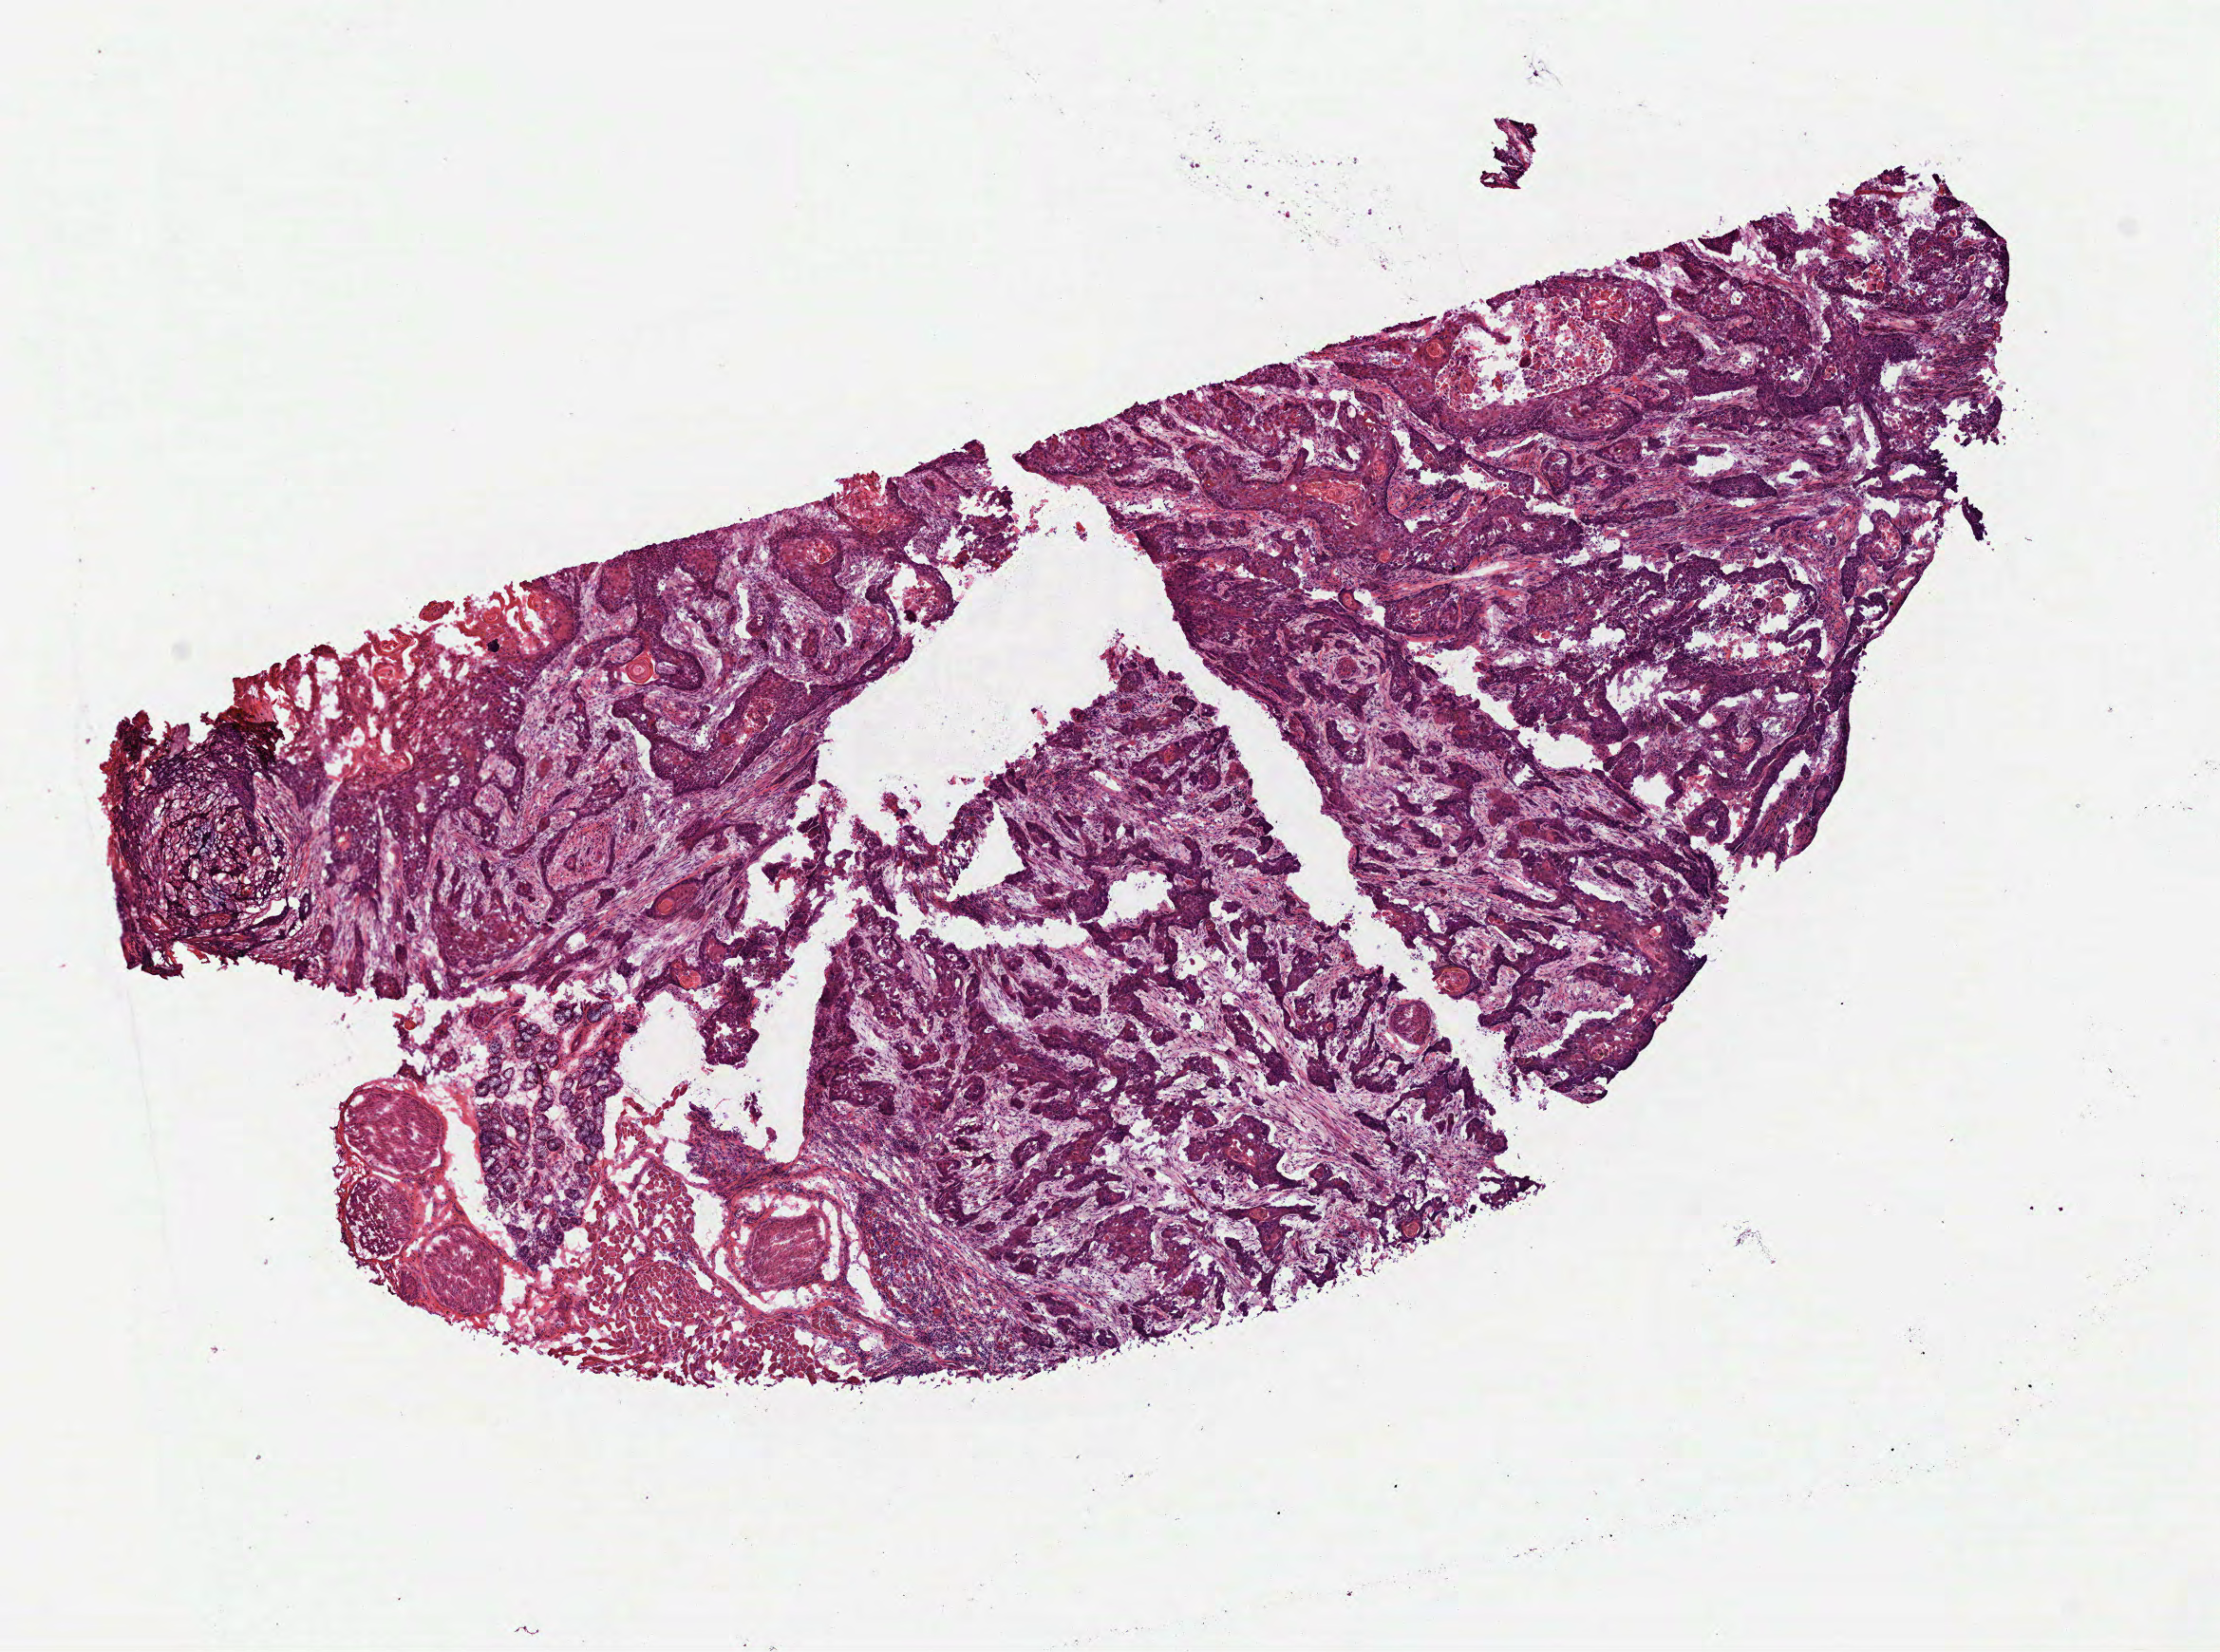
H&E whole-slide image, shown as a low-resolution overview of the whole scanned area (about 9.4 x 7.0 mm, slide scanned at 40x); frozen section from the bottom of the tissue portion; sample: primary tumour, head and neck. Patient: male, age at initial diagnosis 57 years. Histologic grade: G2 (moderately differentiated). Pathologist review of this section (percent, as recorded): tumour cells 82%, tumour nuclei 80%, normal cells 13%, stromal cells 0%, necrosis 5%. Infiltration values recorded for this section: lymphocyte infiltration 10%, monocyte infiltration 0%, neutrophil infiltration 2%.
• AJCC pathologic stage: IVA (7th edition)
• diagnosis: Squamous cell carcinoma, NOS (tongue, NOS)